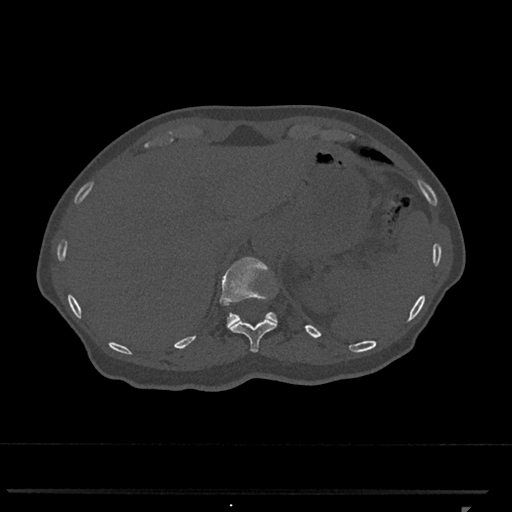
CT including the spine, one axial slice. Position 496 of 793 along the scan axis. Reconstruction kernel Br40s/3. 120 kVp. Bone window (W 1800 / L 400 HU). 0.5 mm slice thickness. 512 × 512 image matrix. Patient: female, 62 years. Case-level facts recorded for this patient, not image findings: primary cancer: renal.
Structures marked on this image (semi-automatic segmentation, software-assisted and operator-edited):
- T11 vertebra: bounding box <227,319,278,352> (left, top, right, bottom; pixels)
- T12 vertebra: <219,257,278,326>